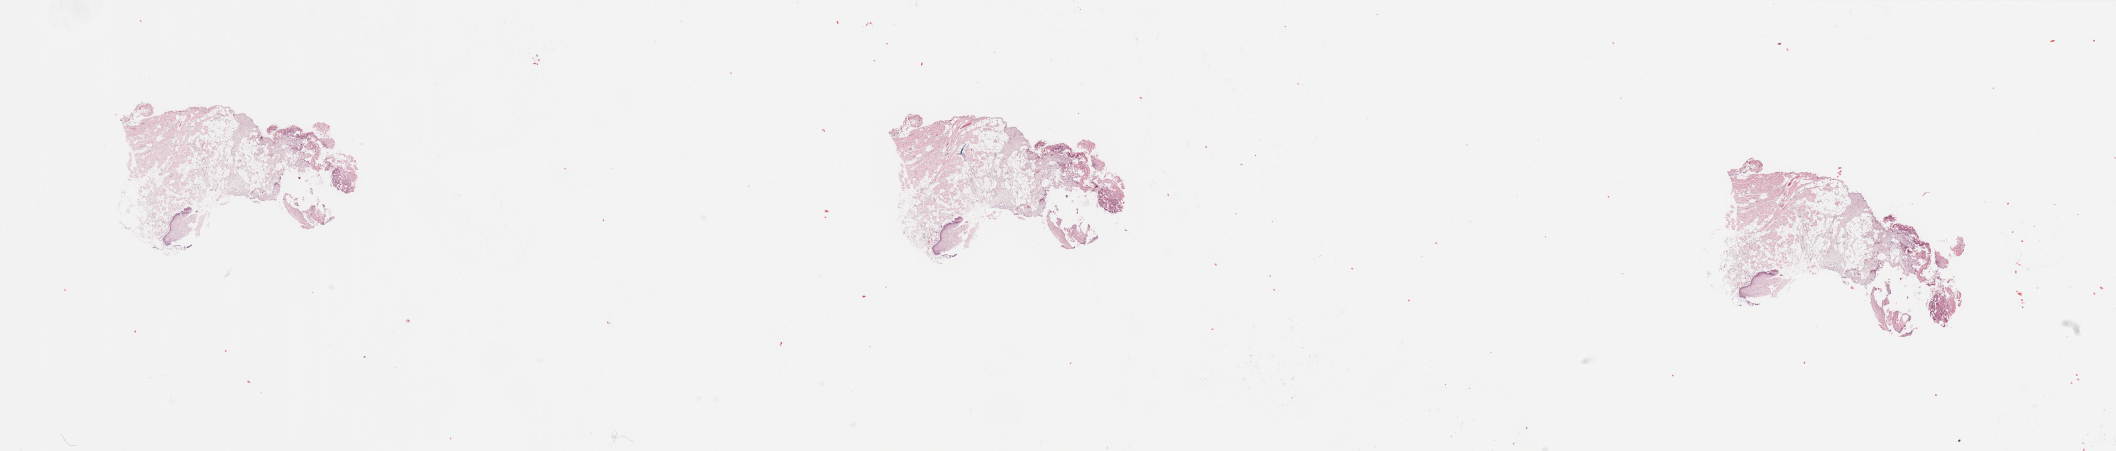
Hematoxylin and eosin (H&E) stained whole-slide image, whole scanned area (about 33.5 x 7.1 mm) shown as a low-resolution overview; head and neck, normal (non-tumour) tissue. Patient: male, age 65 years.
This section: normal (non-tumour) tissue from the same patient. Patient diagnosis: Squamous cell carcinoma, NOS (floor of mouth, NOS).